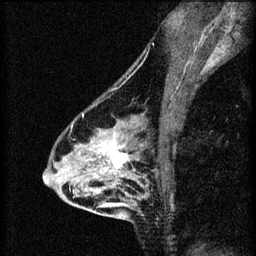
Breast MRI (dynamic contrast-enhanced), one sagittal slice; 3 images stored at this slice position (order not interpretable as contrast timing); 1.5 T; TE 4.2 ms, TR 8.2 ms; 2 mm slice thickness; 256 × 256 image matrix. Patient: female, 46 years.
Outlined on this slice (semi-automatic segmentation, software-assisted and operator-edited):
- analysis volume of interest (the breast-tissue region the enhancement analysis was run in; not a lesion): bounding box [x1, y1, x2, y2] px = [55, 114, 148, 209]
- tumour enhancement mask (voxels above the 70 % enhancement threshold inside the analysis volume of interest): [82, 114, 143, 171]